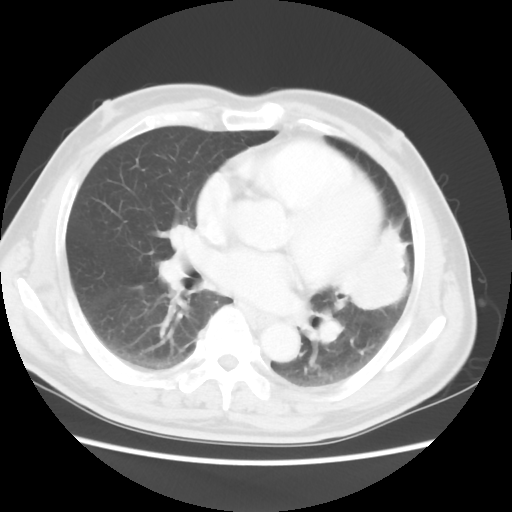
Chest CT, one axial slice; position 24 of 50 along the scan axis; reconstruction kernel STANDARD; lung window (W 1500 / L -600 HU); 512 × 512 image matrix, field of view 360 × 360 mm. Male patient, age 69 years. From the clinical record (not read from this slice): clinical TNM (as recorded): T3 N1 M1a.
Outlined on this slice (bounding box drawn by a radiologist):
- lung tumour (recorded histology: squamous cell carcinoma): bounding box [x1, y1, x2, y2] px = [339, 218, 419, 318]